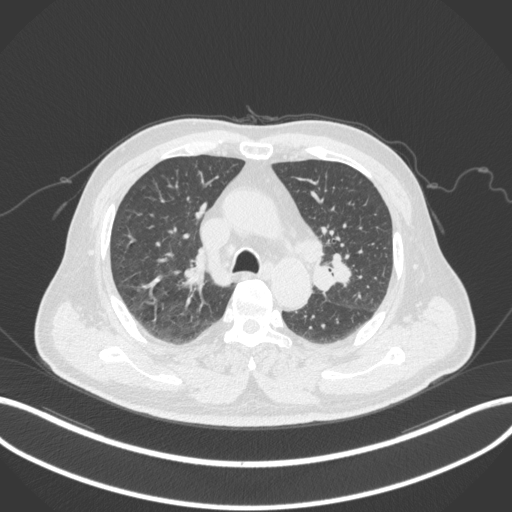
Chest CT, one axial slice; slice 202 of 286 in the series (ordered by position); reconstruction kernel B31f; 120 kVp; lung window (W 1500 / L -600 HU); 1 mm slice thickness; 512 × 512 image matrix, field of view 400 × 400 mm. Male patient, age 67 years. From the clinical record (not read from this slice): clinical TNM (as recorded): T2a N1 M0.
Structures marked on this image (rectangle marked by the reading radiologist):
- lung tumour (recorded histology: adenocarcinoma): bounding box [x1, y1, x2, y2] px = [308, 250, 351, 289]